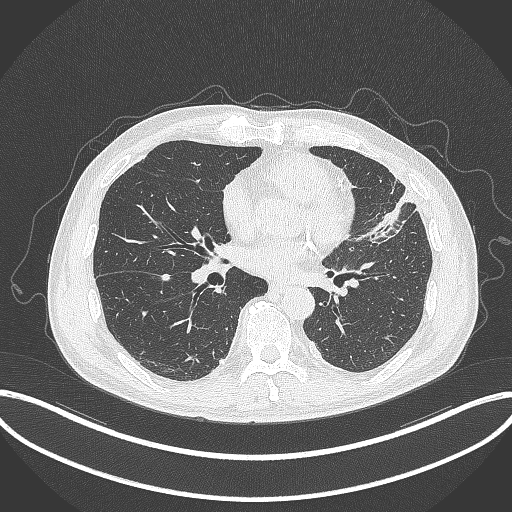
Chest CT, one axial slice; slice 149 of 382 in the series (ordered by position); reconstruction kernel B70f; lung window (W 1500 / L -600 HU); 1 mm slice thickness; 512 × 512 image matrix, field of view 415 × 415 mm. Patient: male, 64 years. Case-level facts recorded for this patient, not image findings: clinical TNM (as recorded): T4 N1 M0; histopathological grade: G3.
Outlined on this slice (bounding box drawn by a radiologist):
- lung tumour (recorded histology: adenocarcinoma): bounding box <357,186,419,243> (left, top, right, bottom; pixels)